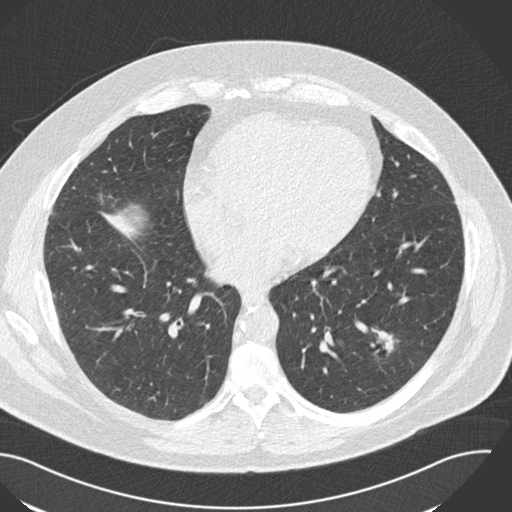
Low-dose screening chest CT, one axial slice. 120 kVp. Lung window (W 1500 / L -600 HU). 512 × 512 image matrix, field of view 394 × 394 mm.
Structures marked on this image (manually delineated by an expert):
- lesion 1 (tumor, lower lobe of left lung): bounding box [x1, y1, x2, y2] px = [371, 331, 394, 353]